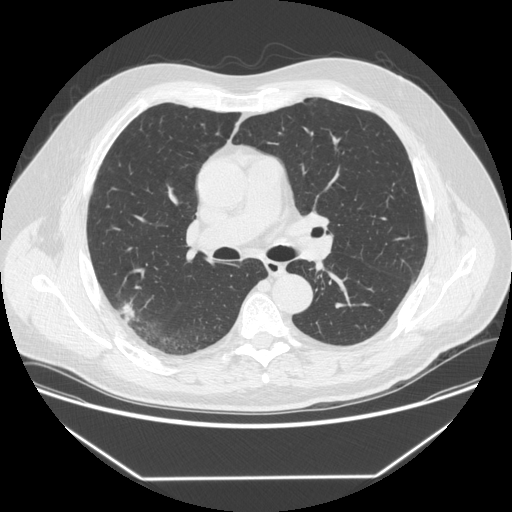
Chest CT (low-dose screening protocol), one axial image. First (baseline) screen. Lung window (W 1500 / L -600 HU). Standard (soft-tissue) reconstruction kernel (STANDARD). Slice 215 of 342 in the series. 512 × 512 image matrix. Male, age 64 years at enrolment.
Lesion marked by an expert reader, bounding box [x1, y1, x2, y2] px = [103, 299, 145, 334]. The exam's reader record, not a measurement of the box and not confirmed to be the same lesion: non-calcified nodule or mass ≥4 mm, right upper lobe, 12 × 12 mm, smooth margins, soft tissue attenuation. Lung cancer was diagnosed 92 days after this screen: adenocarcinoma, NOS, right upper lobe, poorly differentiated (G3), stage IIIB (AJCC 6th edition), 15 mm at pathology.